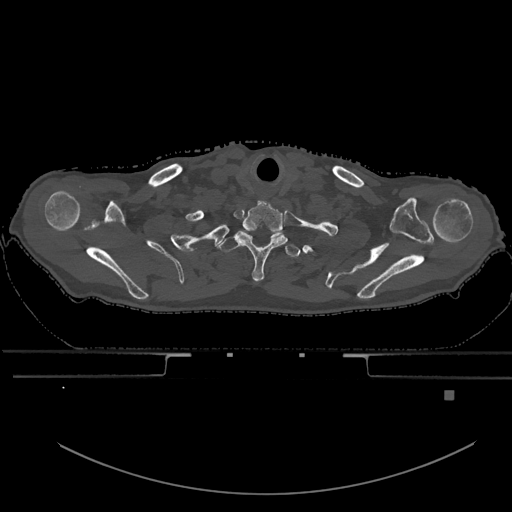
CT including the spine, one axial slice; position 561 of 969 along the scan axis; bone window (W 1800 / L 400 HU); 0.5 mm slice thickness; 512 × 512 image matrix, field of view 456 × 456 mm. Male patient, age 82 years. Case-level facts recorded for this patient, not image findings: primary cancer: prostate; vertebrae with lytic lesions (as recorded): T11, T9, T8, T2.
Annotated regions visible in this slice (semi-automatically segmented with operator editing):
- T1 vertebra: bounding box [x1, y1, x2, y2] px = [218, 234, 300, 258]